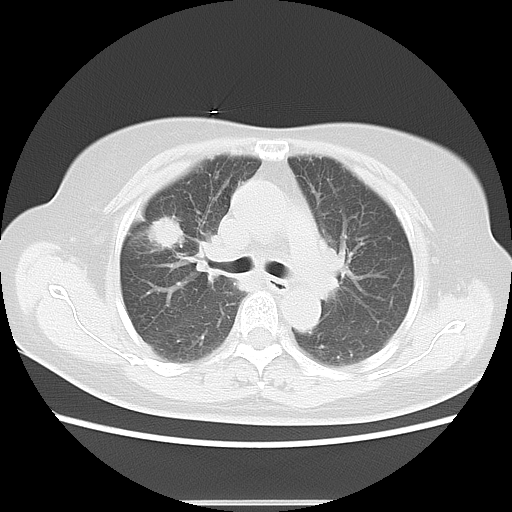
Chest CT, one axial slice. Position 9 of 17 along the scan axis. 120 kVp. Lung window (W 1500 / L -600 HU). 5 mm slice thickness. 512 × 512 image matrix. Patient: female, 57 years. Case-level facts recorded for this patient, not image findings: clinical TNM (as recorded): T1c N1 M0.
Annotated regions visible in this slice (rectangle marked by the reading radiologist):
- lung tumour (recorded histology: adenocarcinoma): bounding box <142,213,187,253> (left, top, right, bottom; pixels)